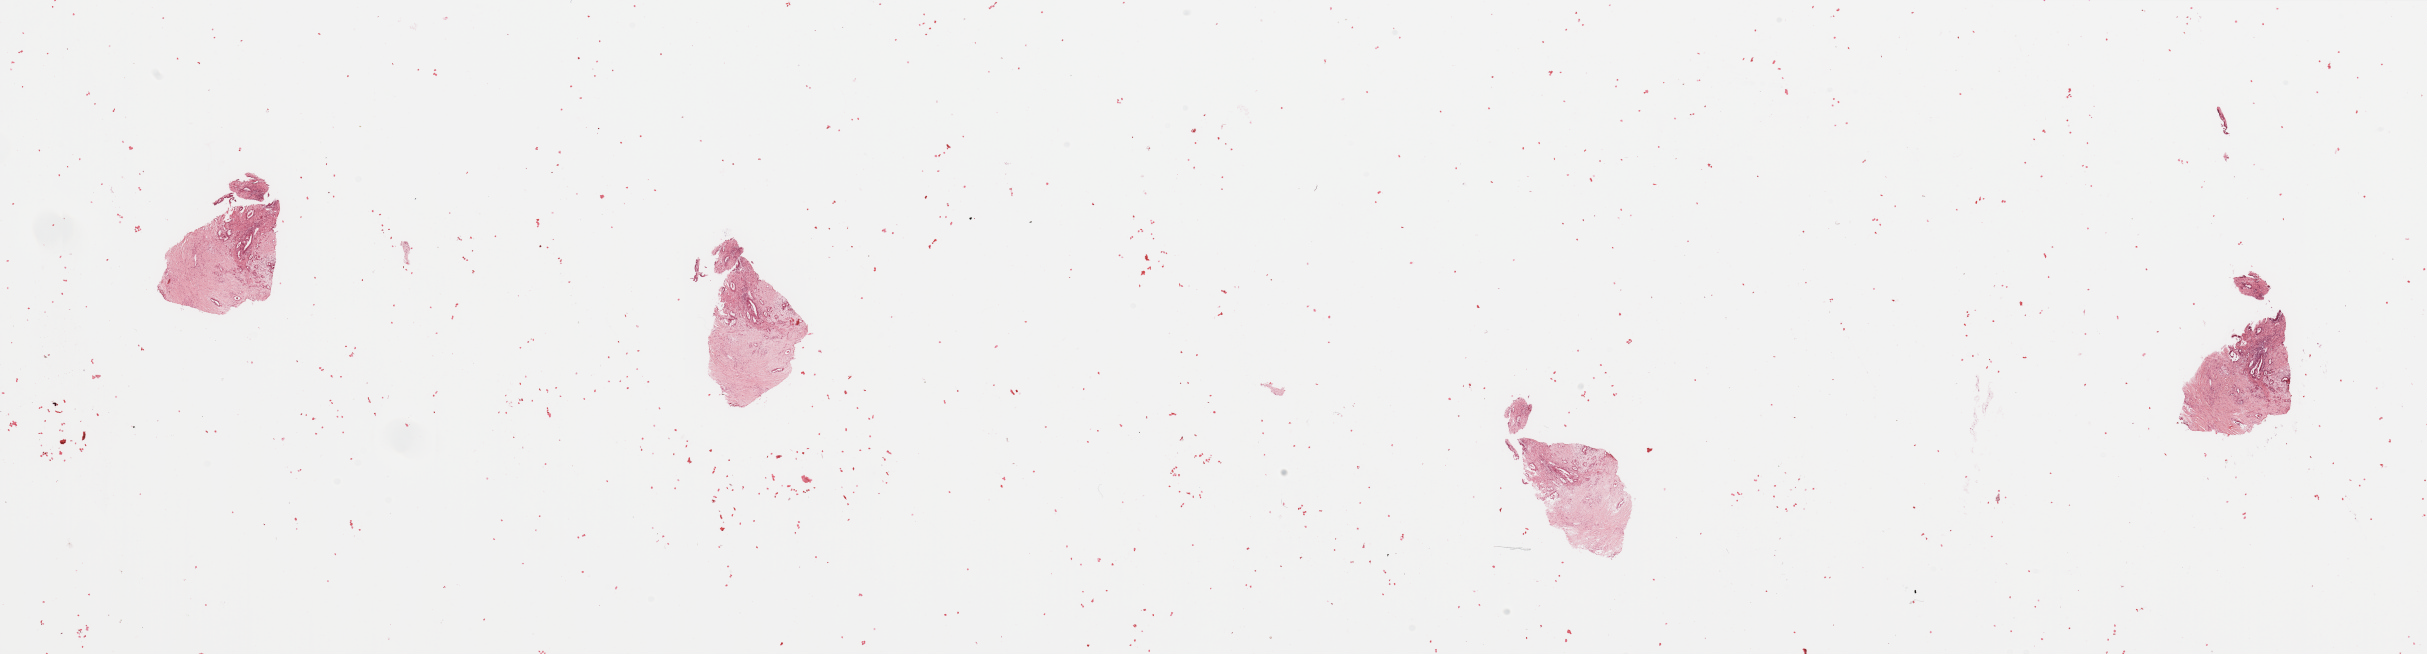
Digitized Hematoxylin and eosin (H&E) stained tissue section (whole slide) — a low-resolution overview of the entire scanned area, about 38.4 x 10.3 mm. Tumour tissue sample, pancreas. Patient: male, age 63 years. Histologic grade: G2 (moderately differentiated).
* histologic diagnosis: Infiltrating duct carcinoma, NOS
* AJCC pathologic stage: IIB
* primary tumour site (as recorded): head